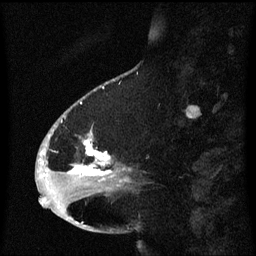
Breast MRI (dynamic contrast-enhanced), one sagittal slice. Slice 22 of 60 in the series (ordered by position). Dynamic contrast-enhanced series, image 2 of 3 at this slice position (ordered by acquisition). 1.5 T. TE 4.2 ms, TR 8.4 ms. 256 × 256 image matrix. Female patient, age 53 years. Case-level facts recorded for this patient, not image findings: setting: breast cancer imaged before/during neoadjuvant chemotherapy; receptor status: HR-positive, HER2-negative.
Outlined on this slice (semi-automatic segmentation, software-assisted and operator-edited):
- analysis volume of interest (the breast-tissue region the enhancement analysis was run in; not a lesion): bounding box <49,108,133,201> (left, top, right, bottom; pixels)
- tumour enhancement mask (voxels above the 70 % enhancement threshold inside the analysis volume of interest): <70,140,112,177>